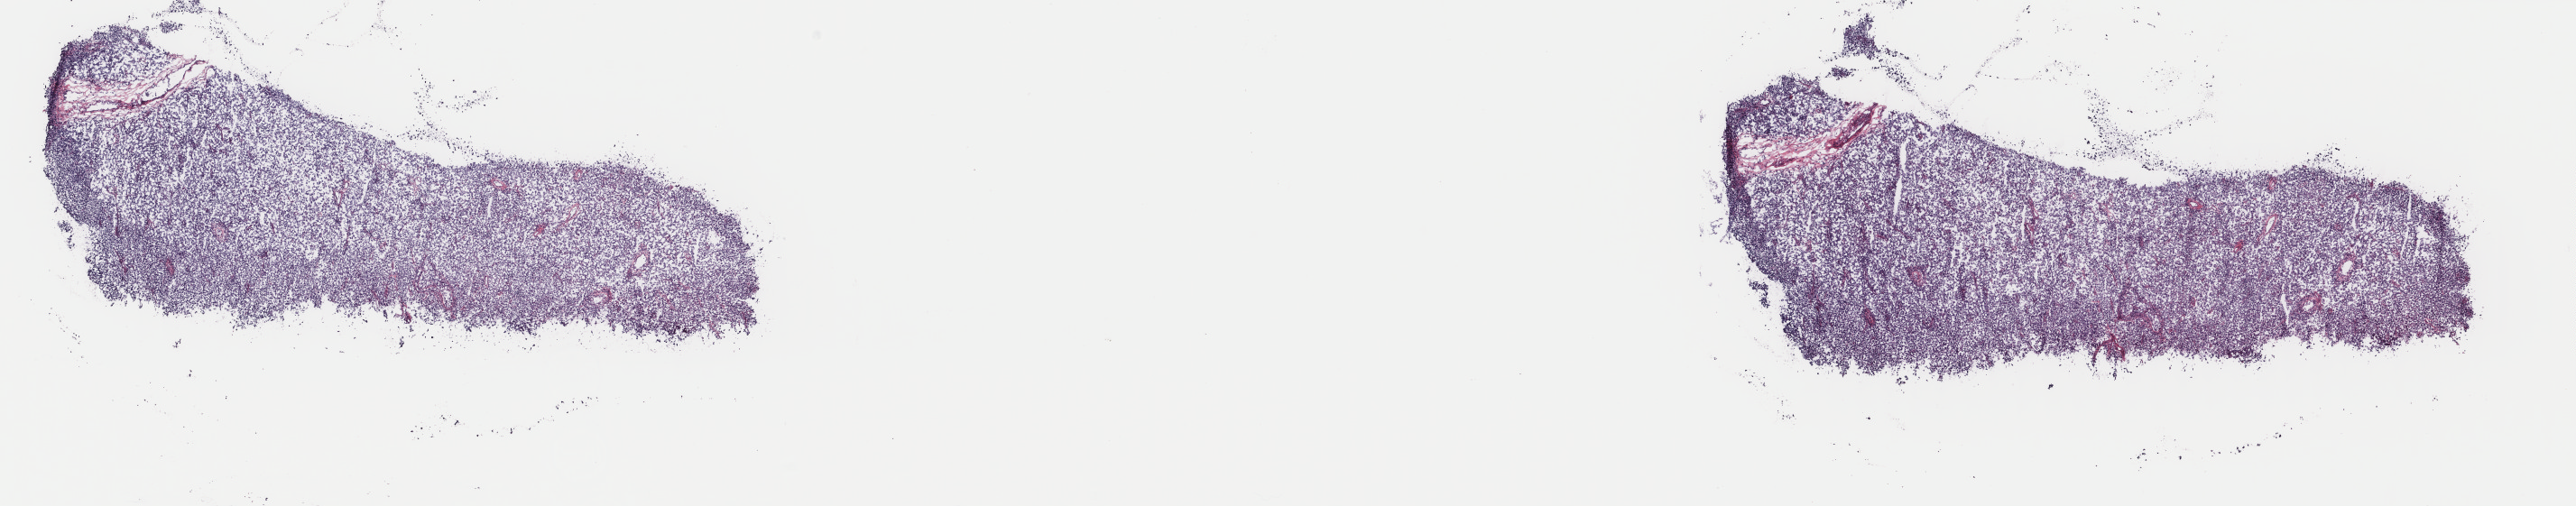
H&E-stained whole-slide image, a low-resolution overview of the entire scanned area, about 22.7 x 4.5 mm, frozen section from the top of the tissue portion, testis, primary tumour sample. Male patient; age at initial diagnosis 22 years. Pathologist review of this section (percent, as recorded): tumour cells 100%, tumour nuclei 70%, normal cells 0%, stromal cells 0%, necrosis 0%. Inflammatory infiltration, as recorded: lymphocyte infiltration 10%, monocyte infiltration 0%, neutrophil infiltration 1%.
Diagnosis: Seminoma, NOS. AJCC pathologic stage: IA (7th edition). Laterality: right.